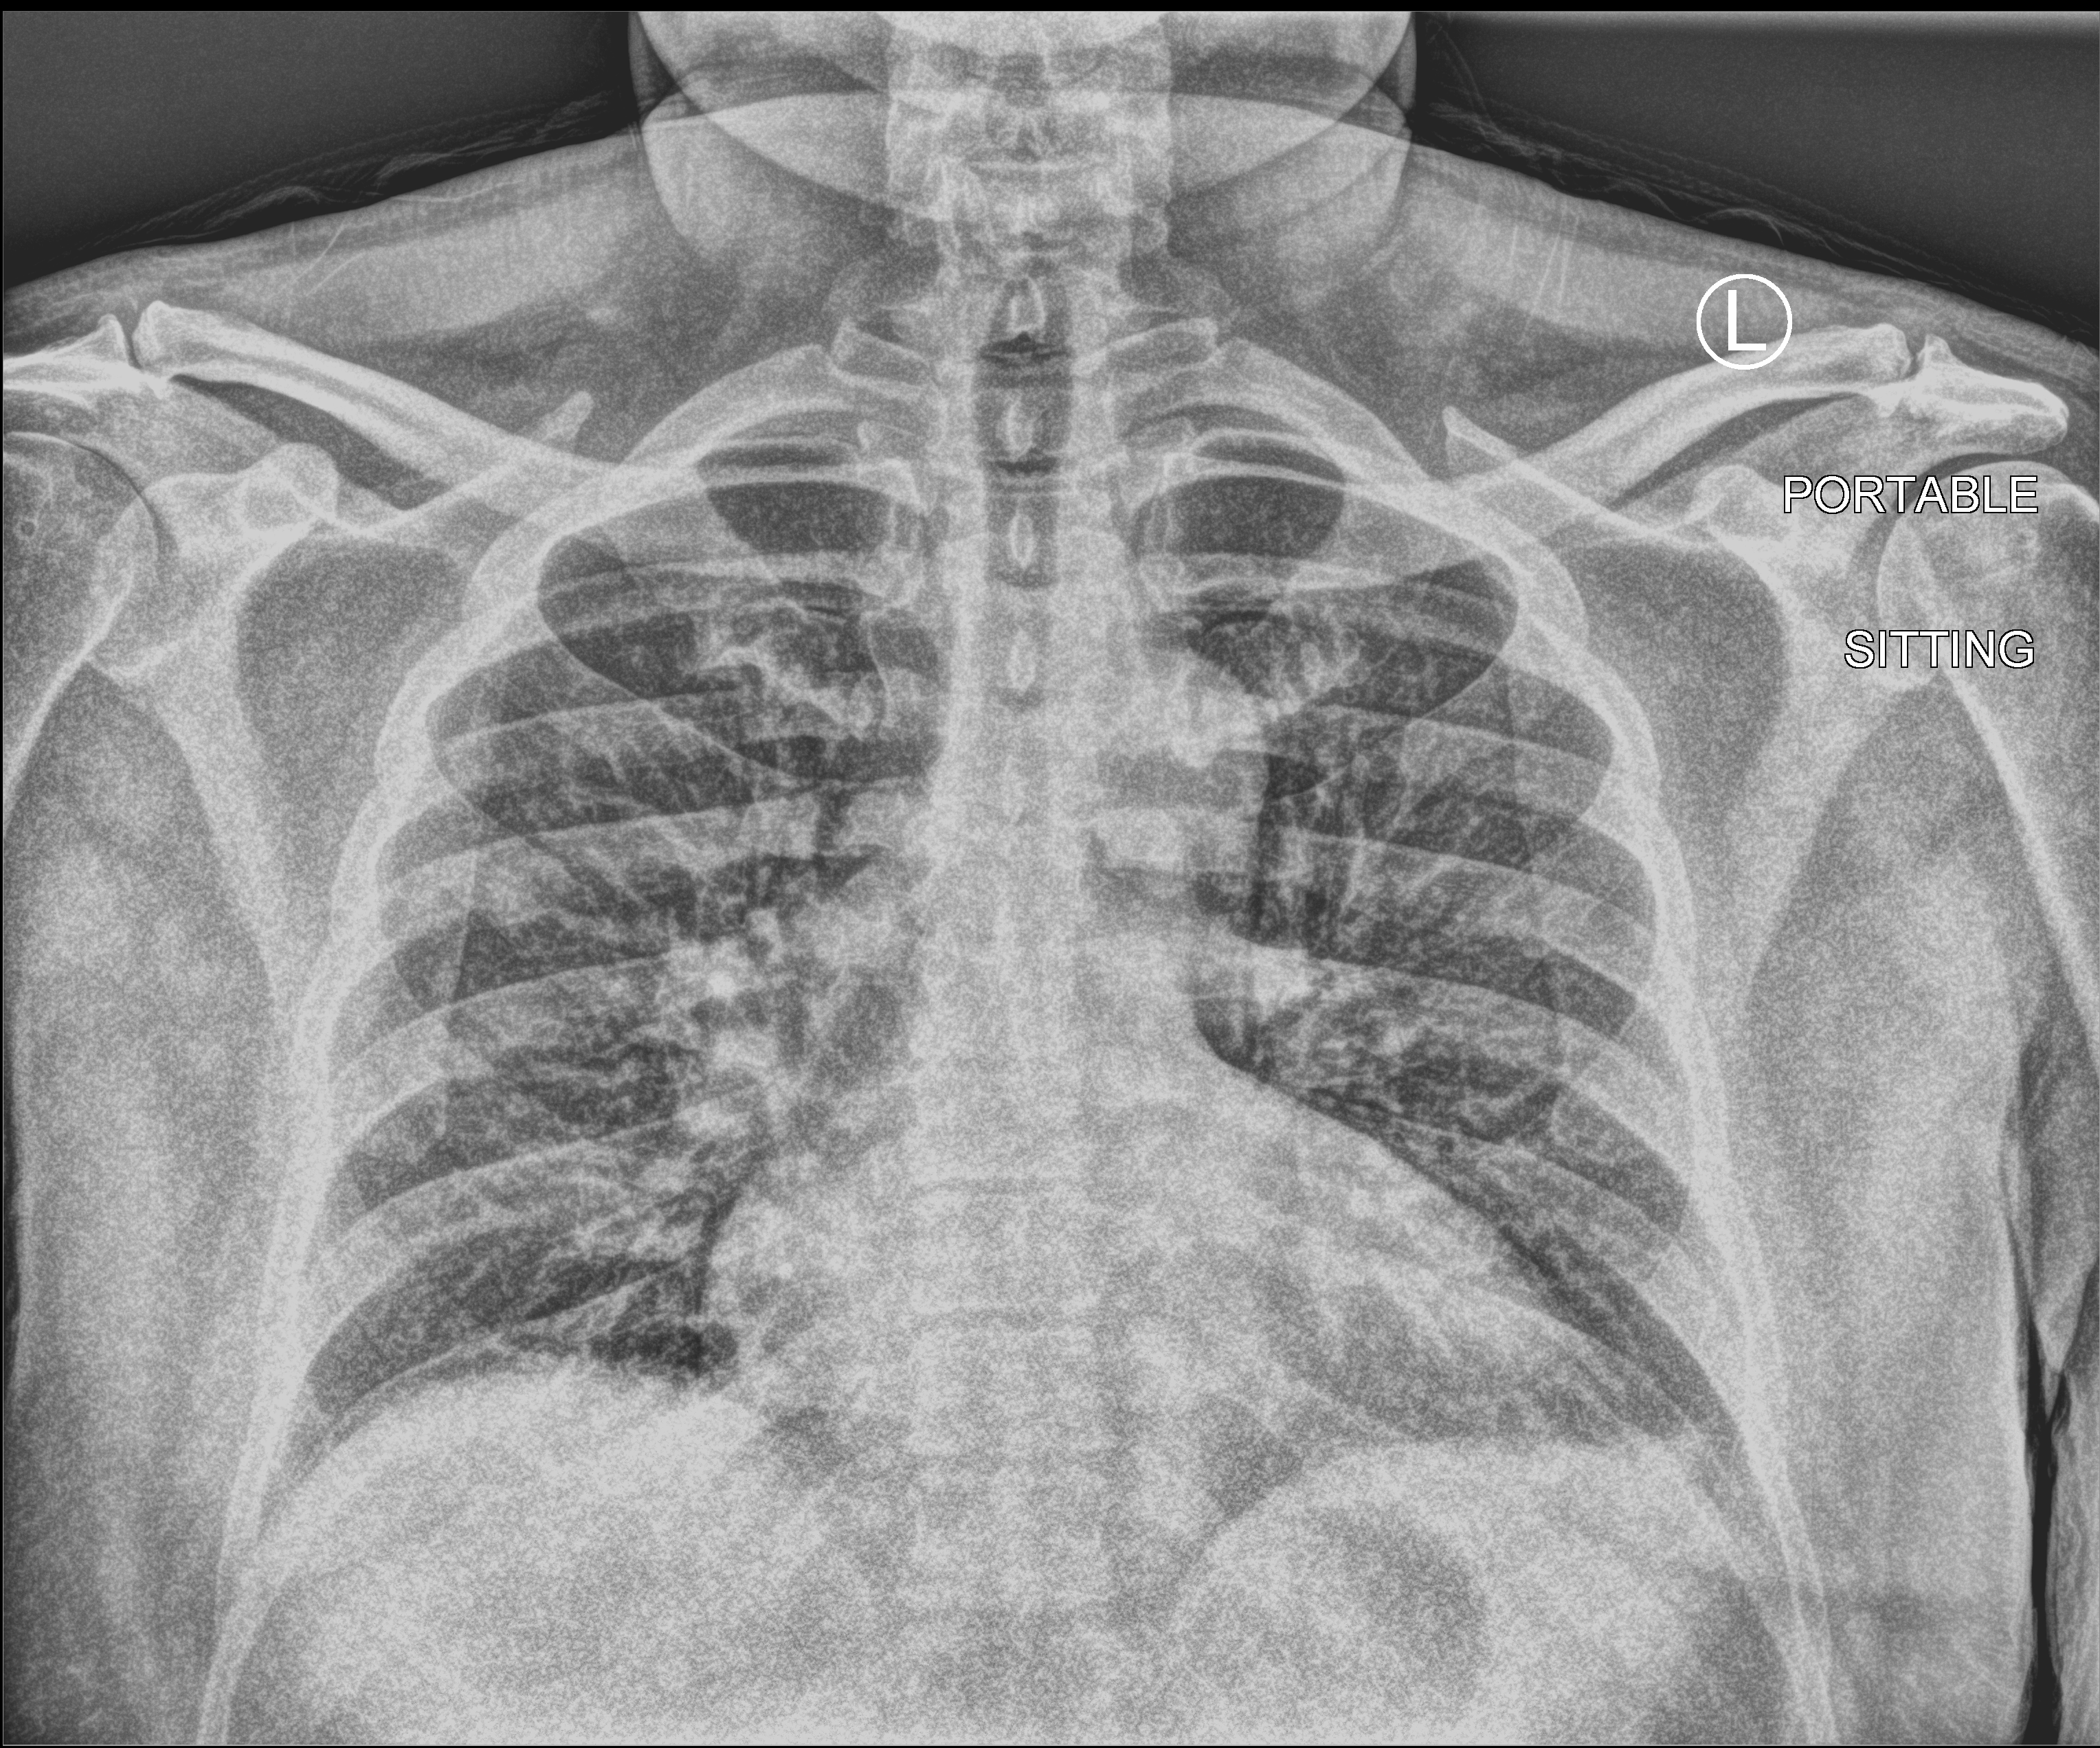
Chest X-ray (portable); anteroposterior (AP) projection. Male patient hospitalised with COVID-19, age 18–59 years.
From the hospital-stay record, not from the radiograph (when in the stay this image was taken is not recorded):
- admitted to intensive care during this hospital stay: no
- hypertension (admission record): no